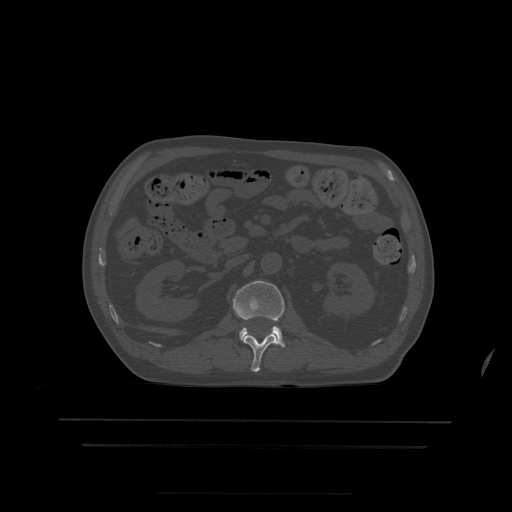
CT including the spine, one axial slice; position 157 of 522 along the scan axis; bone window (W 1800 / L 400 HU); 512 × 512 image matrix, field of view 436 × 436 mm. Patient age 68 years. From the clinical record (not read from this slice): primary cancer: urothelial.
Annotated regions visible in this slice (semi-automatically segmented with operator editing):
- L1 vertebra: bounding box (x1, y1, x2, y2) in pixels: (244, 333, 277, 372)
- L2 vertebra: (233, 281, 286, 347)